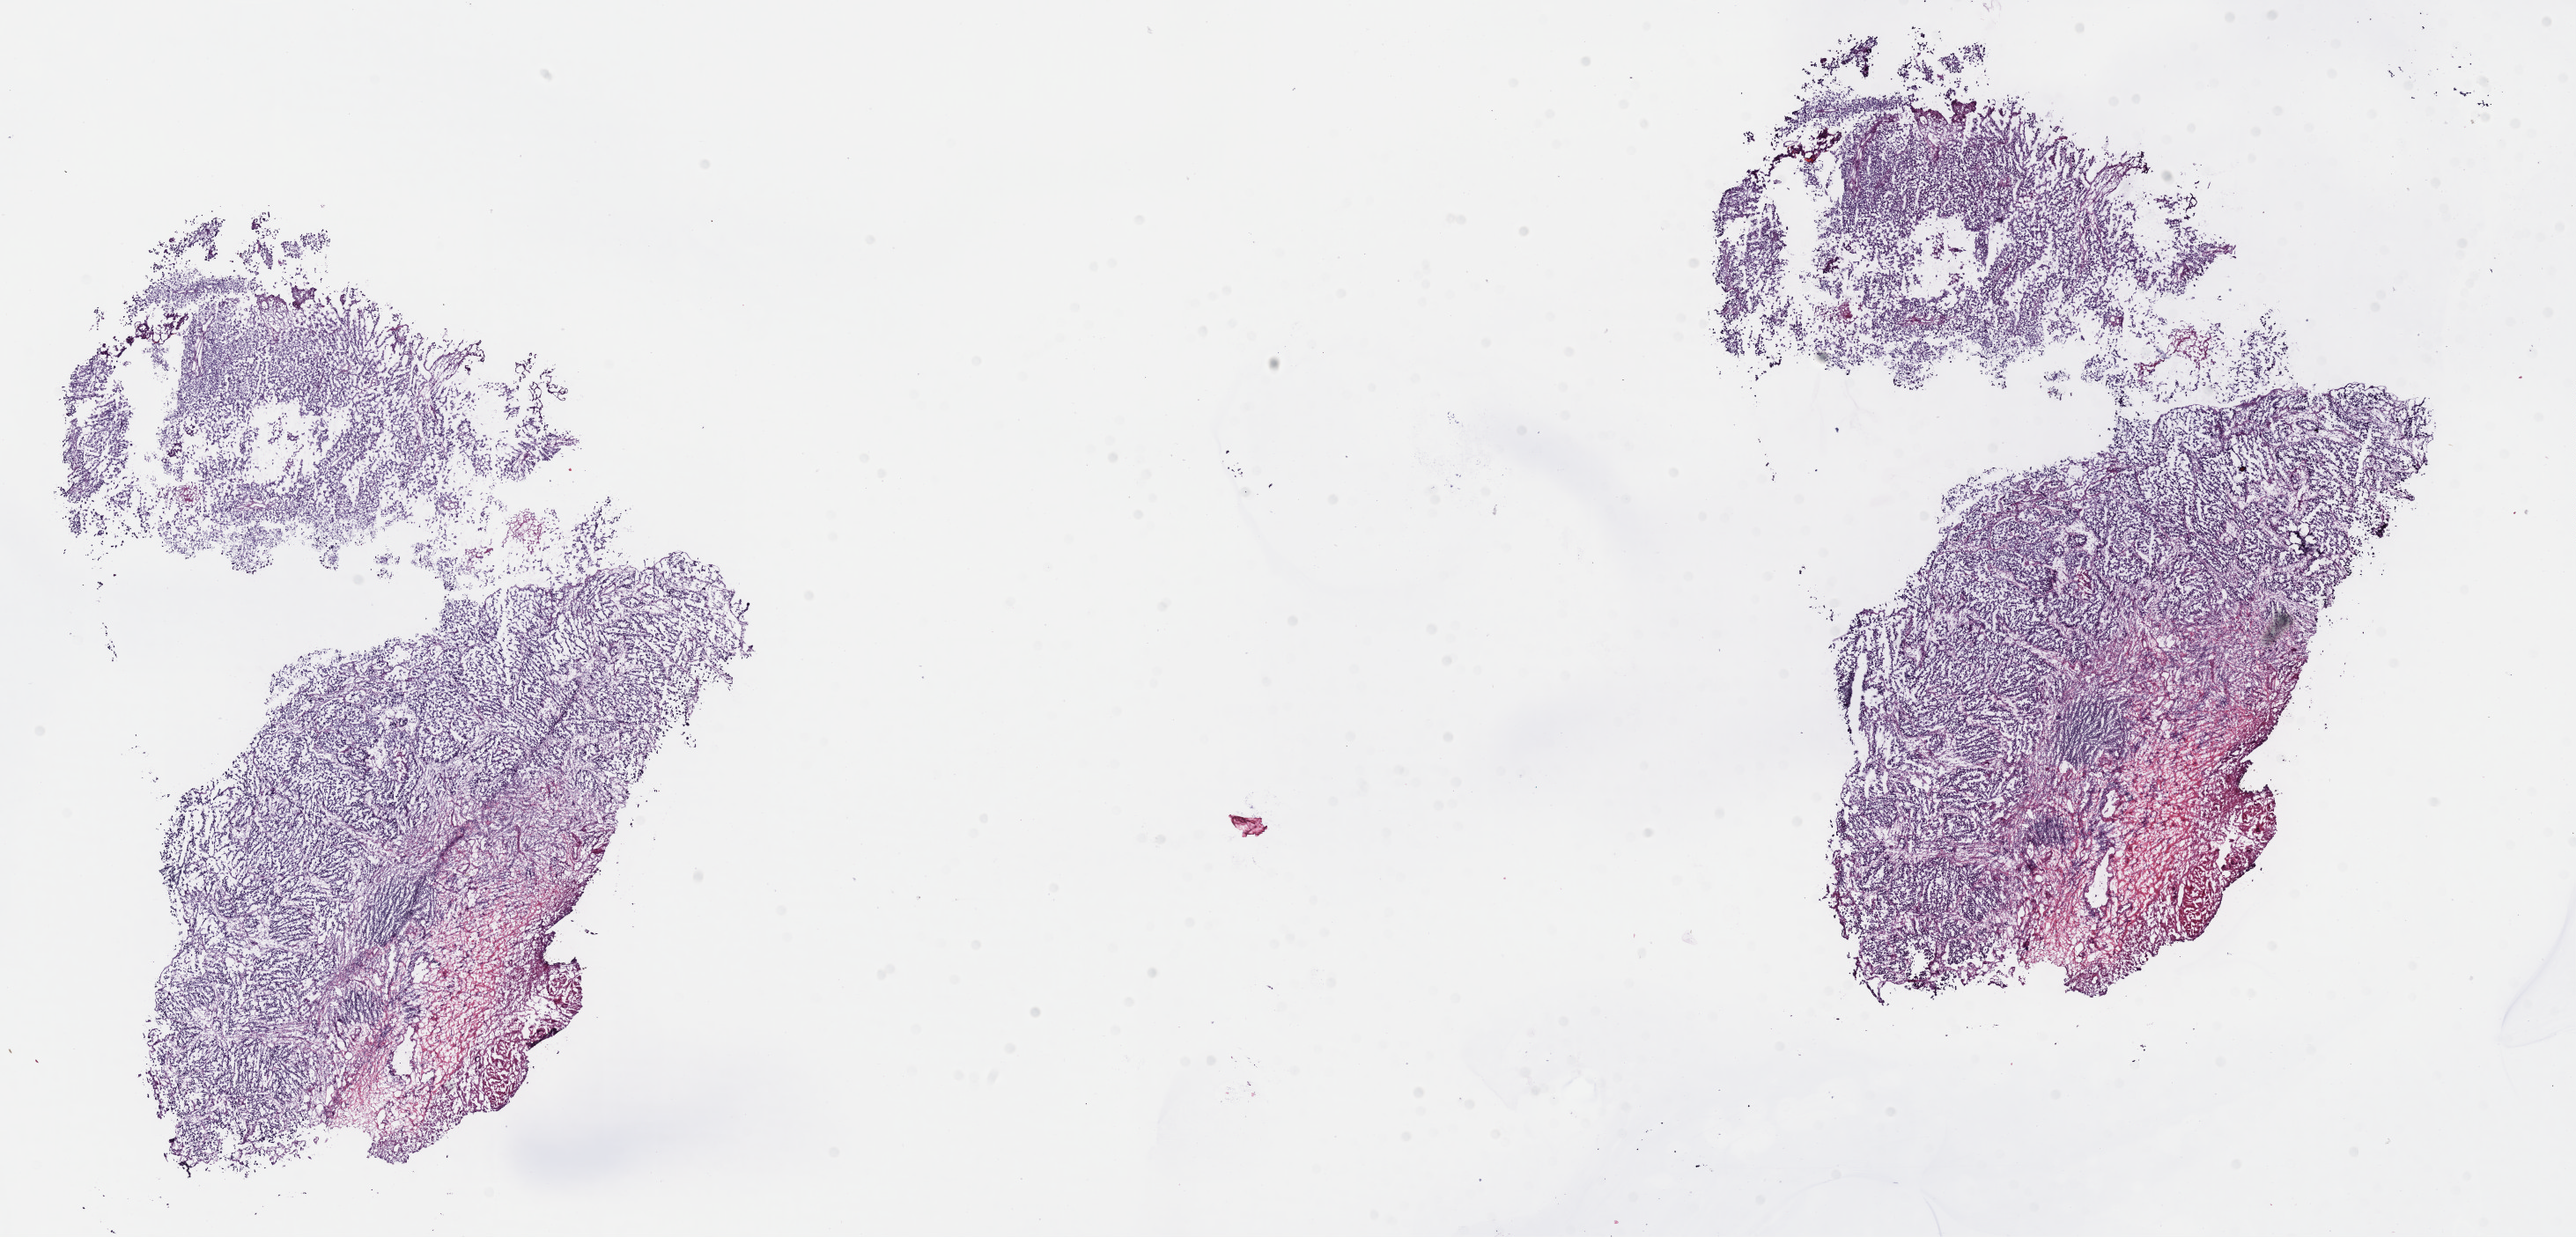
Whole-slide histology image, H&E-stained — whole scanned area (about 23.7 x 11.4 mm, slide scanned at 40x) shown as a low-resolution overview; frozen section from the top of the tissue portion; bladder, primary tumour sample. Female patient; age at initial diagnosis 72 years. Histologic grade: high grade. Pathologist review of this section (percent, as recorded): tumour cells 80%, tumour nuclei 70%, normal cells 20%, stromal cells 0%, necrosis 0%. Infiltration values recorded for this section: lymphocyte infiltration 3%, monocyte infiltration 0%, neutrophil infiltration 0%.
Histologic diagnosis: Transitional cell carcinoma. AJCC pathologic stage: II (7th edition). TNM: N0 M0.